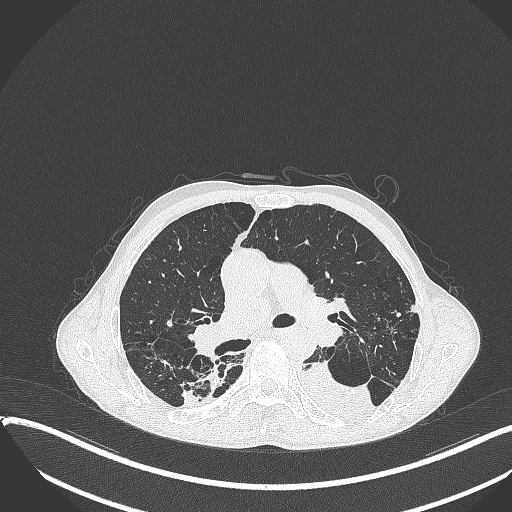
Chest CT, one axial slice; position 233 of 401 along the scan axis; reconstruction kernel B70f; 120 kVp; lung window (W 1500 / L -600 HU); 1 mm slice thickness; 512 × 512 image matrix, field of view 400 × 400 mm. Patient: male, 57 years. Case-level facts recorded for this patient, not image findings: clinical TNM (as recorded): T4 N0 M0.
Annotated regions visible in this slice (rectangle marked by the reading radiologist):
- lung tumour (recorded histology: squamous cell carcinoma): bounding box <295,357,376,422> (left, top, right, bottom; pixels)